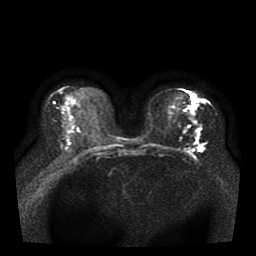
Breast MRI, one axial slice. Slice 18 of 41 in the series (ordered by position). Diffusion-weighted series; image 2 of 4 stored at this slice position (different b-values; order by instance number). 1.5 T. 5 mm slice thickness. 256 × 256 image matrix, field of view 330 × 330 mm. Female patient.
Structures marked on this image (manually delineated by an expert):
- tumour on diffusion-weighted imaging: box from (x=197, y=99) to (x=204, y=152) px